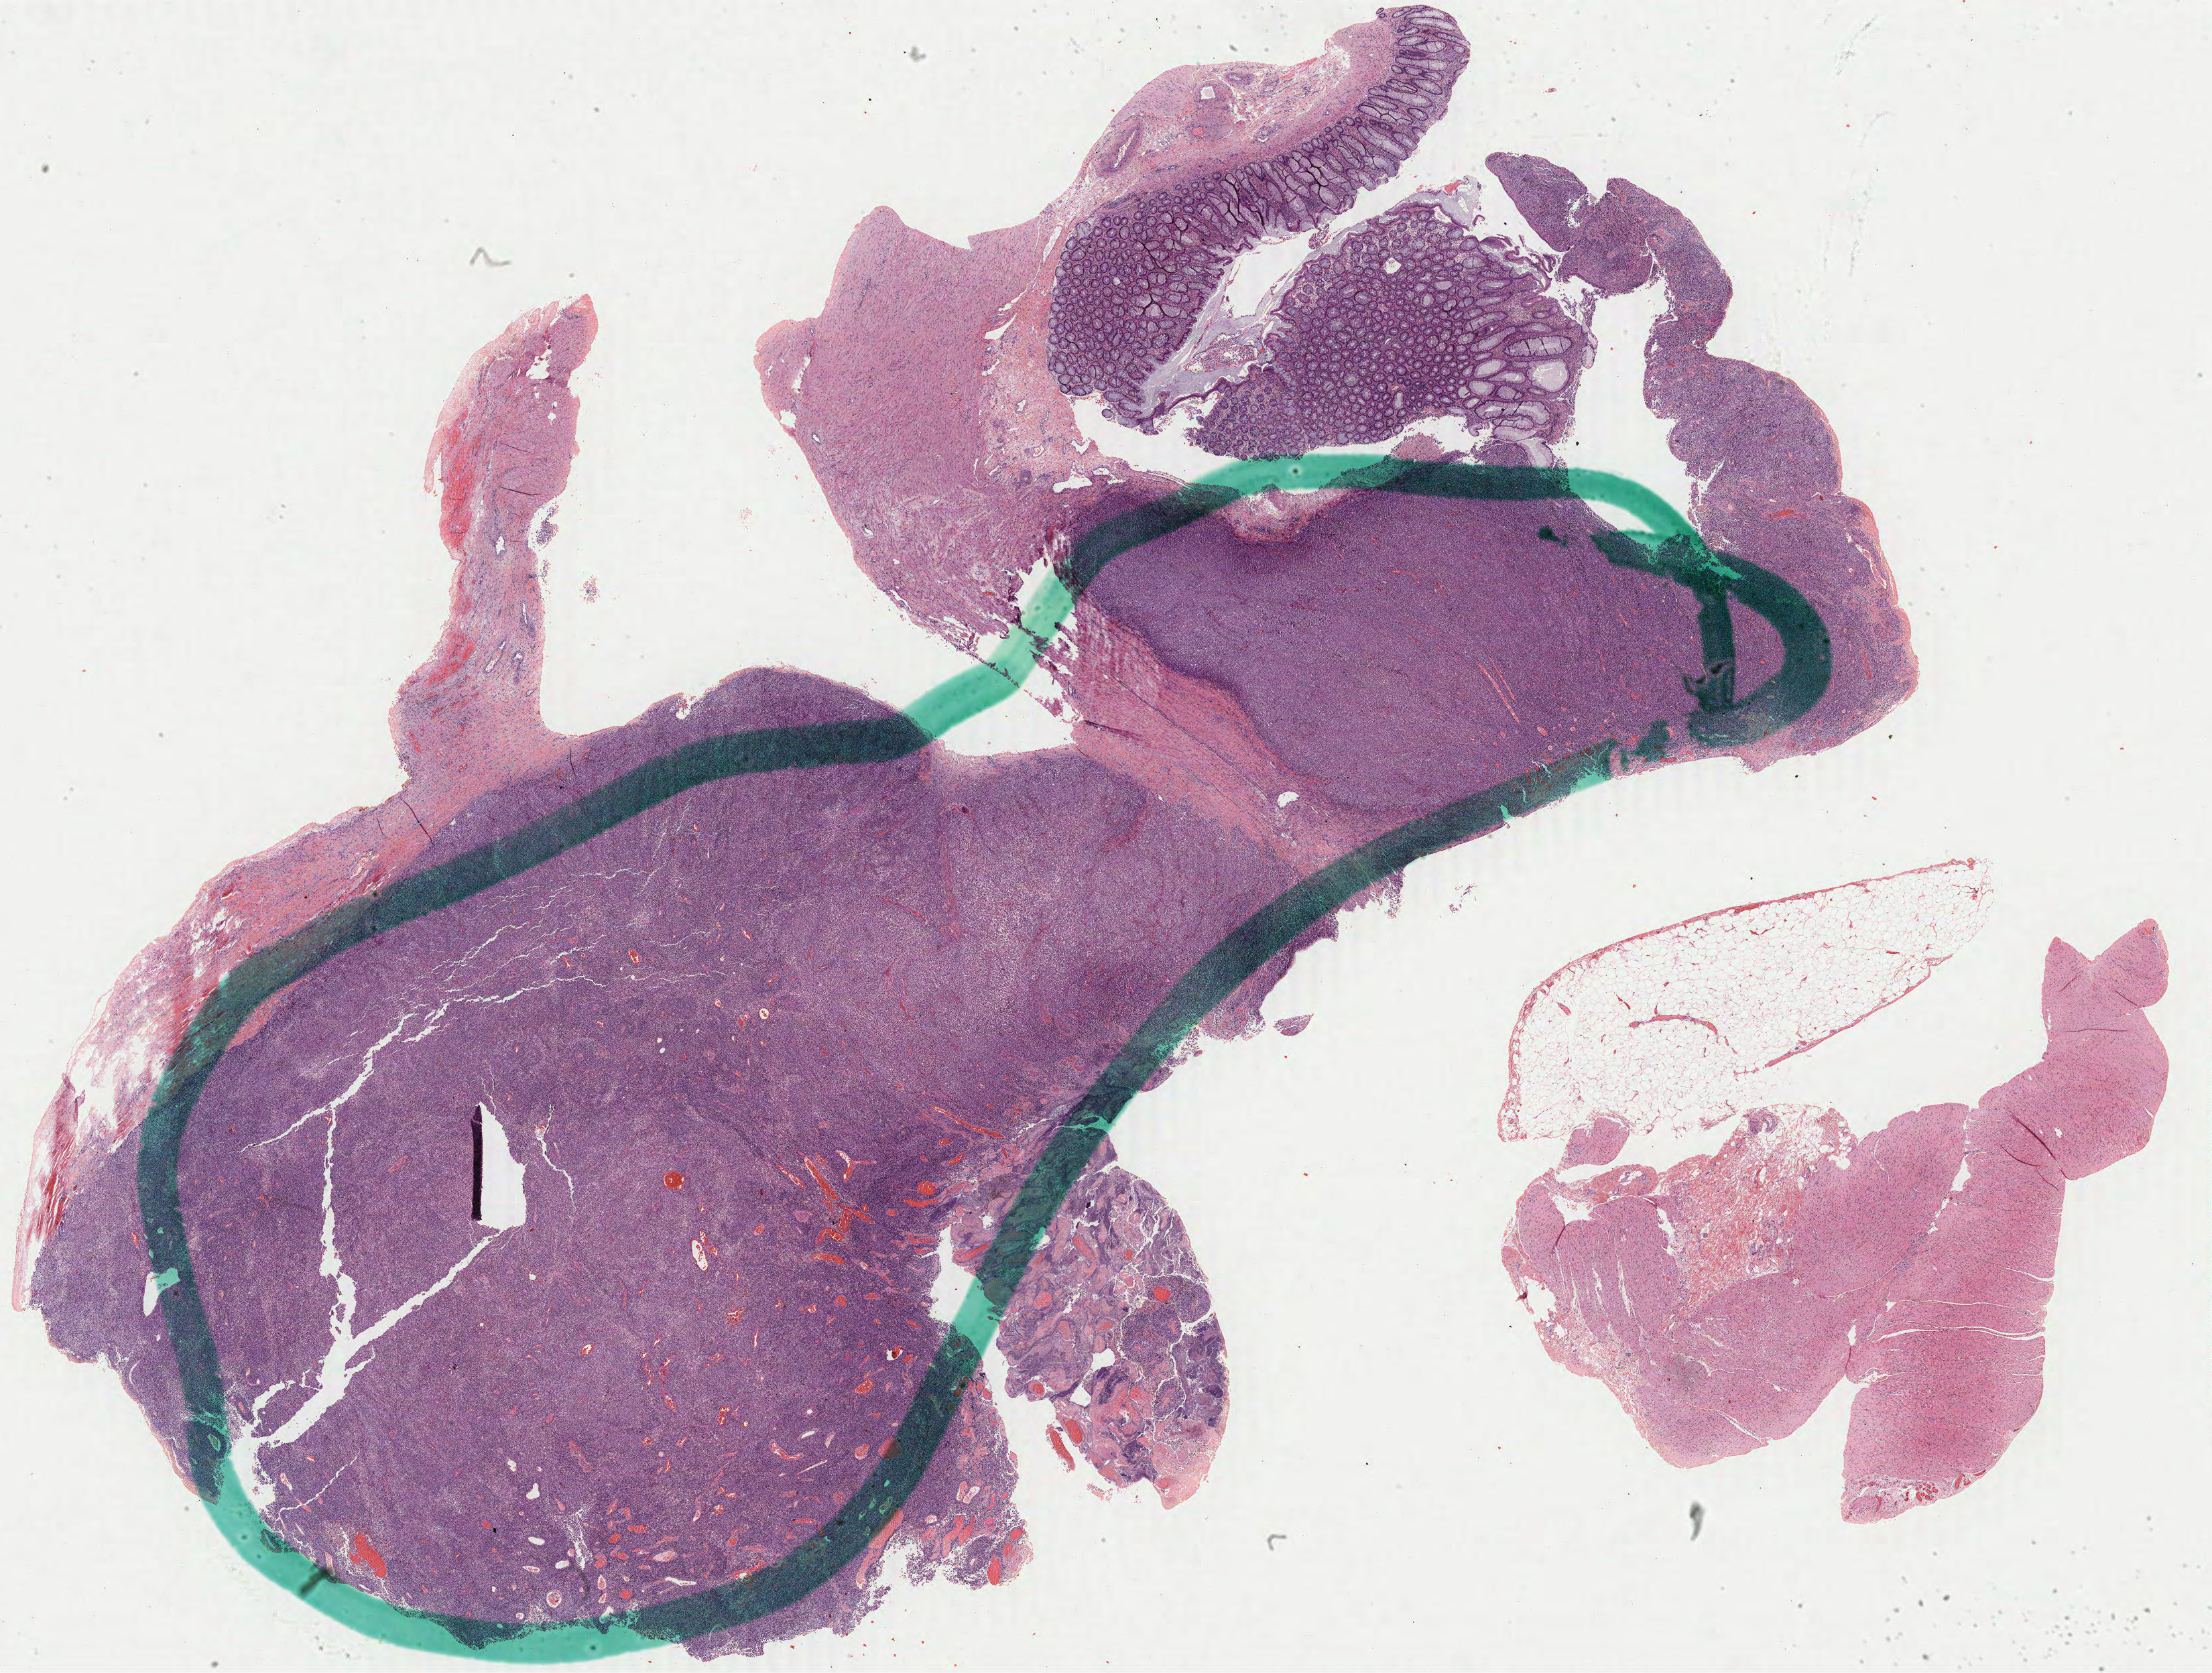
Digitized H&E tissue section (whole slide), shown as a low-resolution overview of the whole scanned area (about 26.5 x 20.0 mm, from a 40x scan). FFPE section. Metastatic tumour sample, sampled site: colon. Patient sex: male.
This section: metastatic tumour tissue. Patient diagnosis: Epithelioid cell melanoma.